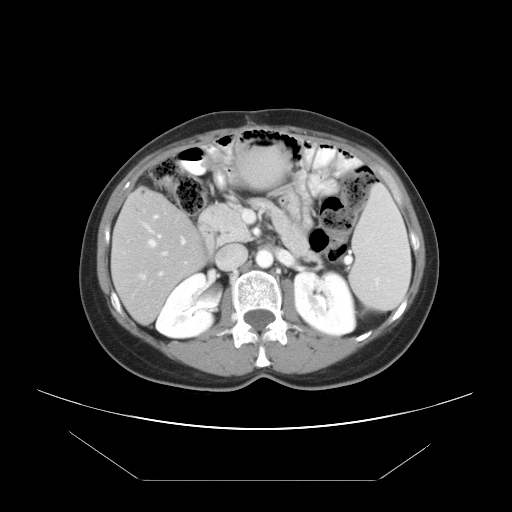
Contrast-enhanced abdominal CT, one axial slice. Slice 20 of 45 in the series (ordered by position). 120 kVp. Intravenous contrast given. Soft-tissue window (W 400 / L 40 HU). 512 × 512 image matrix, field of view 405 × 405 mm. Female patient, age 52 years. From the clinical record (not read from this slice): diagnosis: colorectal cancer liver metastases, imaged before liver resection; multiple liver metastases: yes; largest metastasis: 2.5 cm.
Outlined on this slice (manually delineated by an expert):
- hepatic veins: box from (x=141, y=226) to (x=163, y=278) px
- liver: (x=112, y=192)–(x=203, y=322)
- planned liver remnant (the part of the liver to remain after resection): (x=112, y=192)–(x=202, y=322)
- portal vein (with intrahepatic branches): (x=153, y=214)–(x=186, y=256)